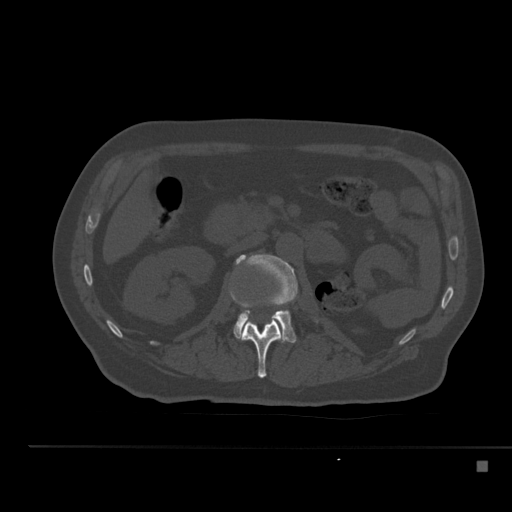
CT including the spine, one axial slice; position 198 of 517 along the scan axis; reconstruction kernel Br40s; bone window (W 1800 / L 400 HU); 1.5 mm slice thickness; 512 × 512 image matrix, field of view 408 × 408 mm. Patient: male, 70 years. From the clinical record (not read from this slice): primary cancer: renal.
Annotated regions visible in this slice (semi-automatically segmented with operator editing):
- L1 vertebra: bounding box <229,289,286,378> (left, top, right, bottom; pixels)
- L2 vertebra: <233,254,298,343>